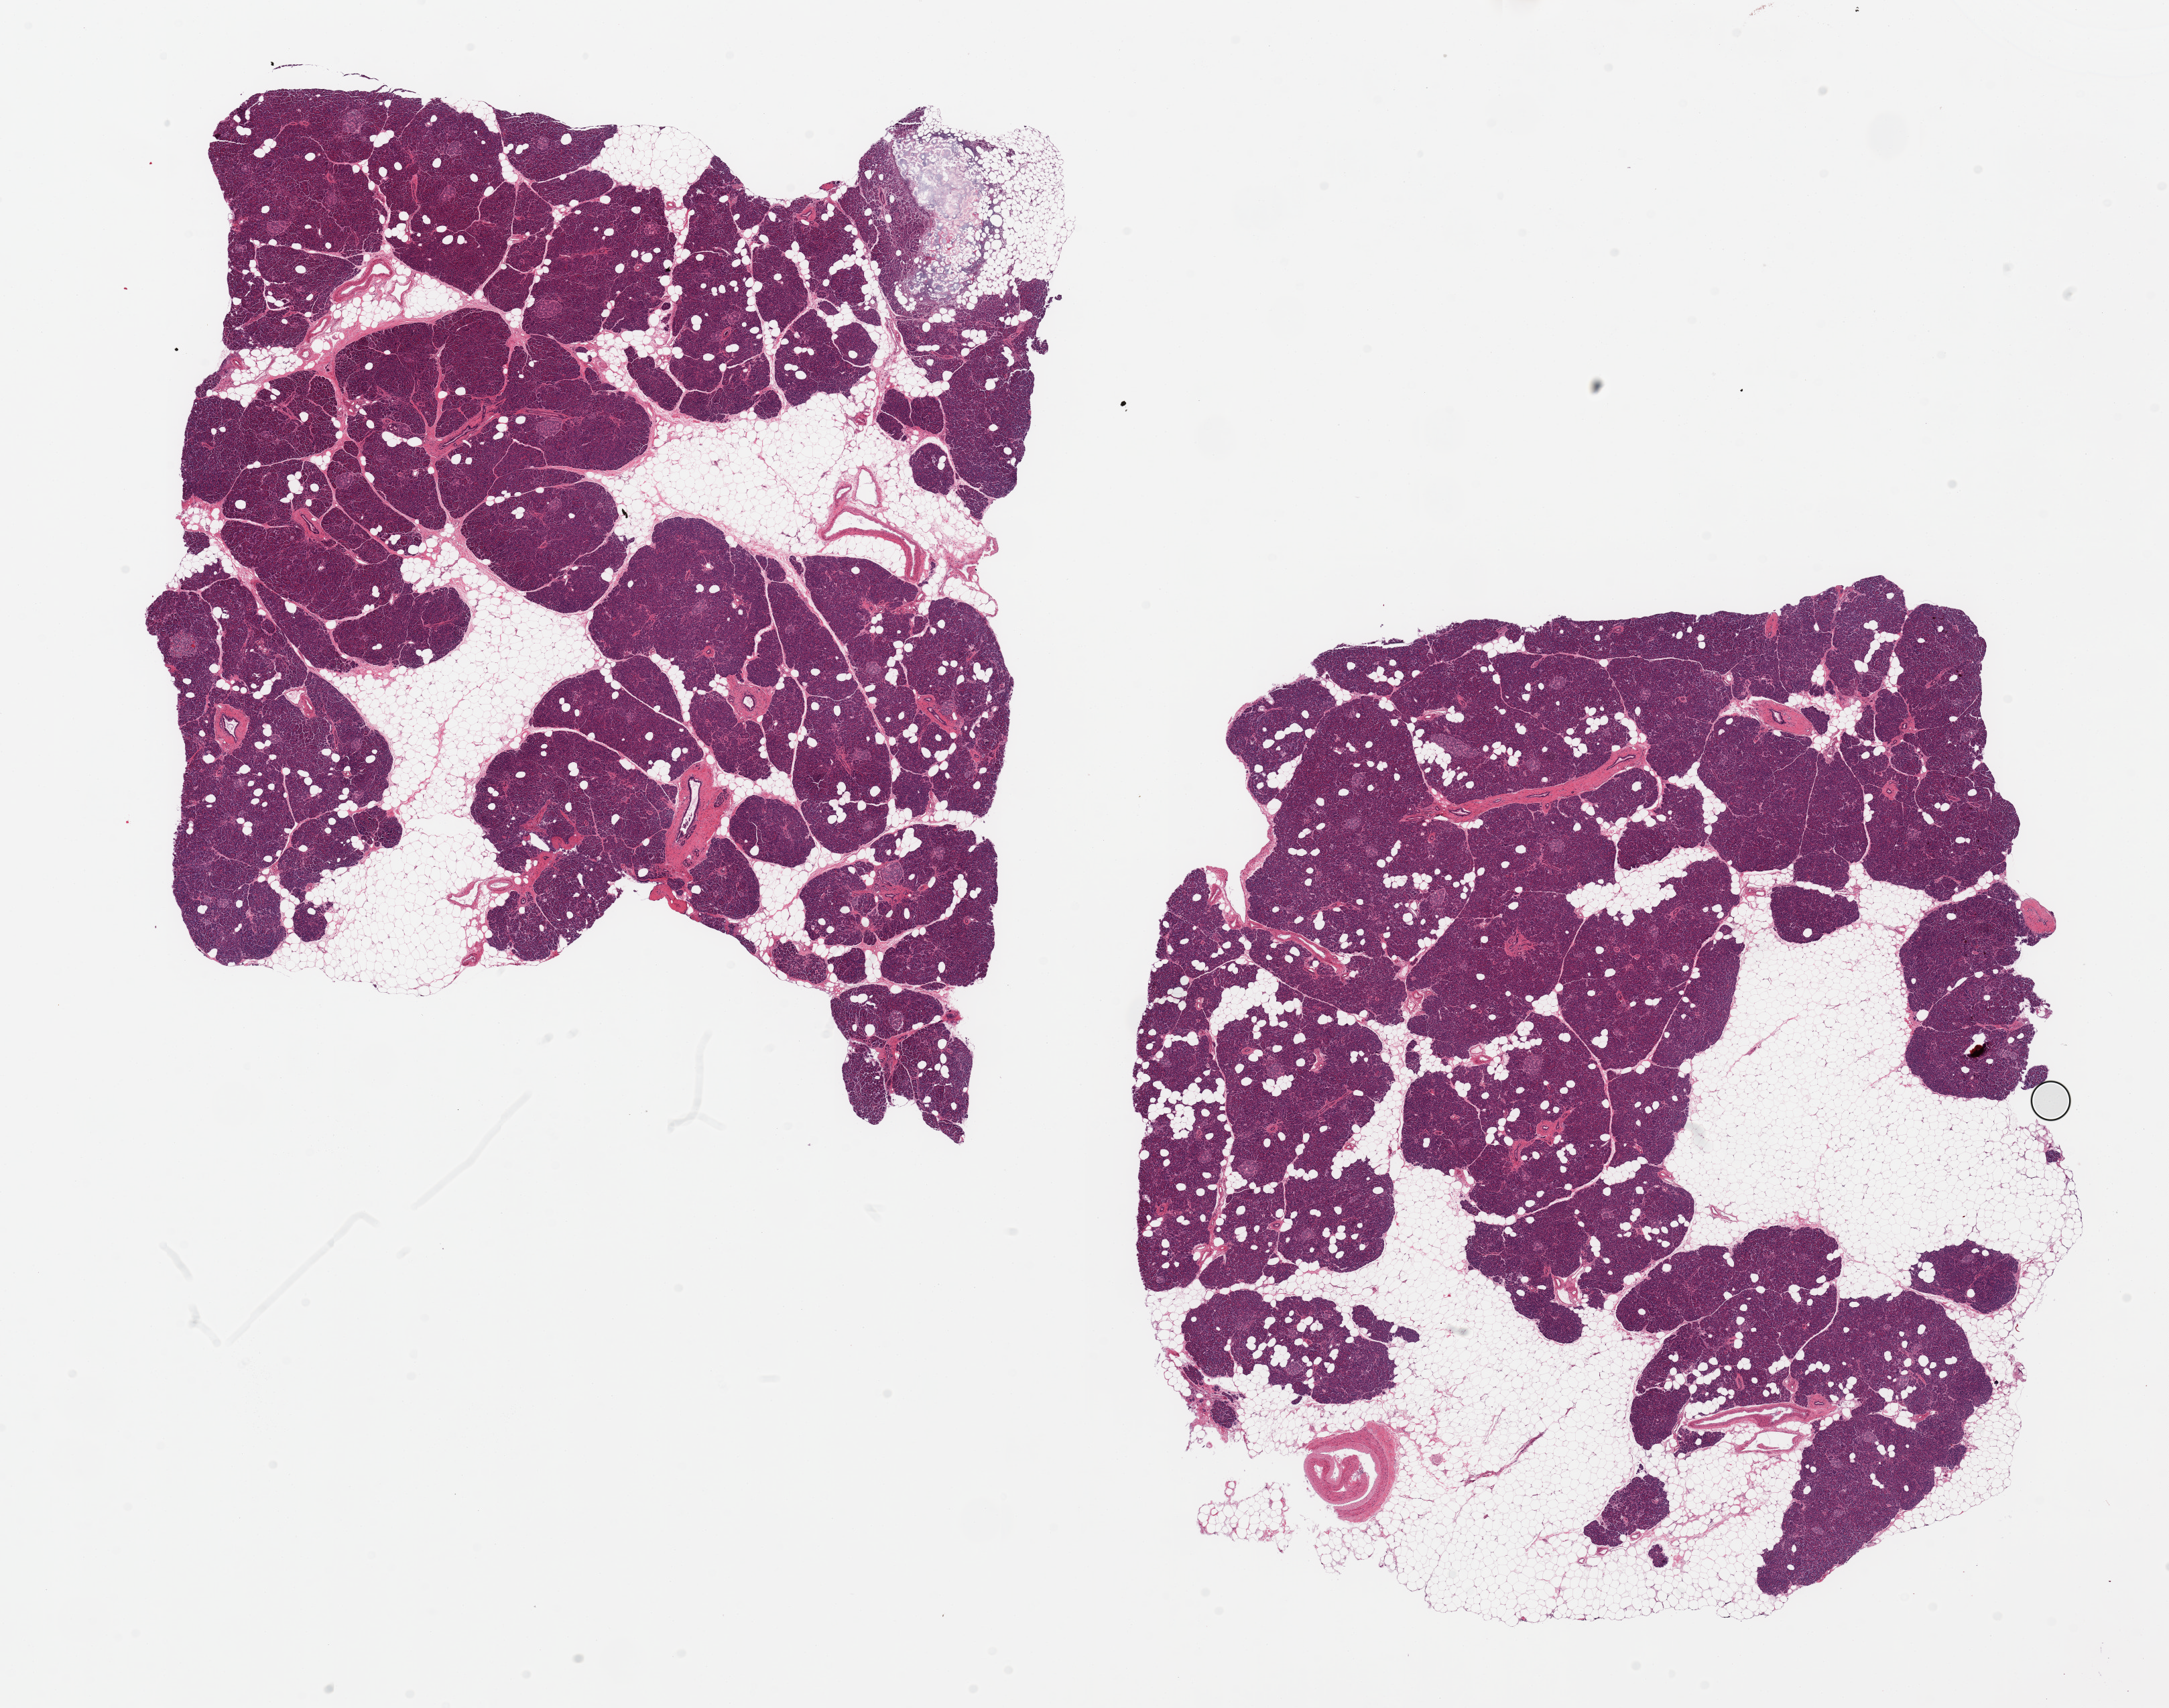
Hematoxylin and eosin (H&E) whole-slide image — whole scanned area (about 25.6 x 20.2 mm, acquisition: 20x scan) shown as a low-resolution overview. PAXgene-fixed paraffin-embedded (PFPE) section. Sampled site (target tissue): pancreas. Donor tissue sample.
Review note (as recorded): 2 pieces, islets well-preserved; ~30% adherent/interstitial fat.